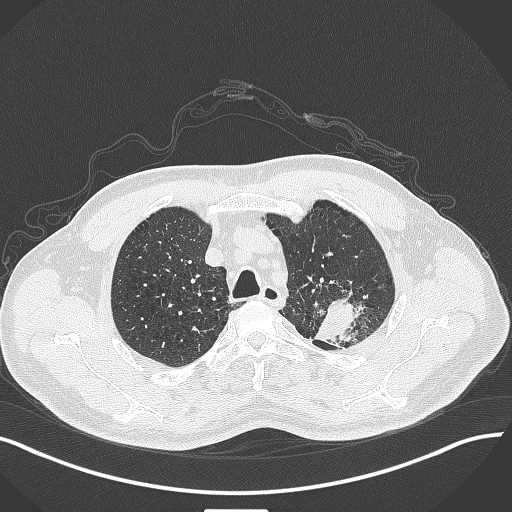
Chest CT, one axial slice; 120 kVp; lung window (W 1500 / L -600 HU); 512 × 512 image matrix, field of view 400 × 400 mm. Male patient, age 55 years. Case-level facts recorded for this patient, not image findings: clinical TNM (as recorded): T3 N0 M1c; histopathological grade: G3.
Structures marked on this image (rectangle marked by the reading radiologist):
- lung tumour (recorded histology: adenocarcinoma): bounding box [x1, y1, x2, y2] px = [308, 293, 380, 351]